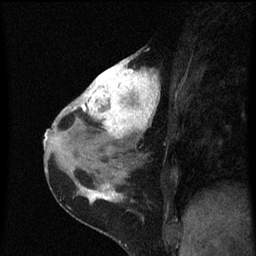
Breast MRI (dynamic contrast-enhanced), one sagittal slice; dynamic contrast-enhanced series, image 2 of 3 at this slice position (ordered by acquisition); 1.5 T; TE 4.2 ms, TR 8 ms; 2 mm slice thickness; 256 × 256 image matrix. Female patient, age 38 years.
Structures marked on this image (semi-automatic segmentation, software-assisted and operator-edited):
- analysis volume of interest (the breast-tissue region the enhancement analysis was run in; not a lesion): box from (x=80, y=52) to (x=161, y=151) px
- tumour enhancement mask (voxels above the 70 % enhancement threshold inside the analysis volume of interest): (x=80, y=58)–(x=161, y=139)